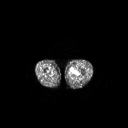
FDG PET of an extremity soft-tissue mass (from a PET/CT study), one axial slice. Slice 224 of 267 in the series (ordered by position). 3.27 mm slice thickness. 128 × 128 image matrix. Male patient, age 63 years. From the clinical record (not read from this slice): histological type: pleiomorphic liposarcoma; grade: high; site of the primary tumour: left thigh.
Outlined on this slice (expert contour drawn on MRI and transferred to this co-registered scan by the dataset authors):
- gross tumour volume including surrounding oedema: bounding box [x1, y1, x2, y2] px = [72, 68, 79, 75]